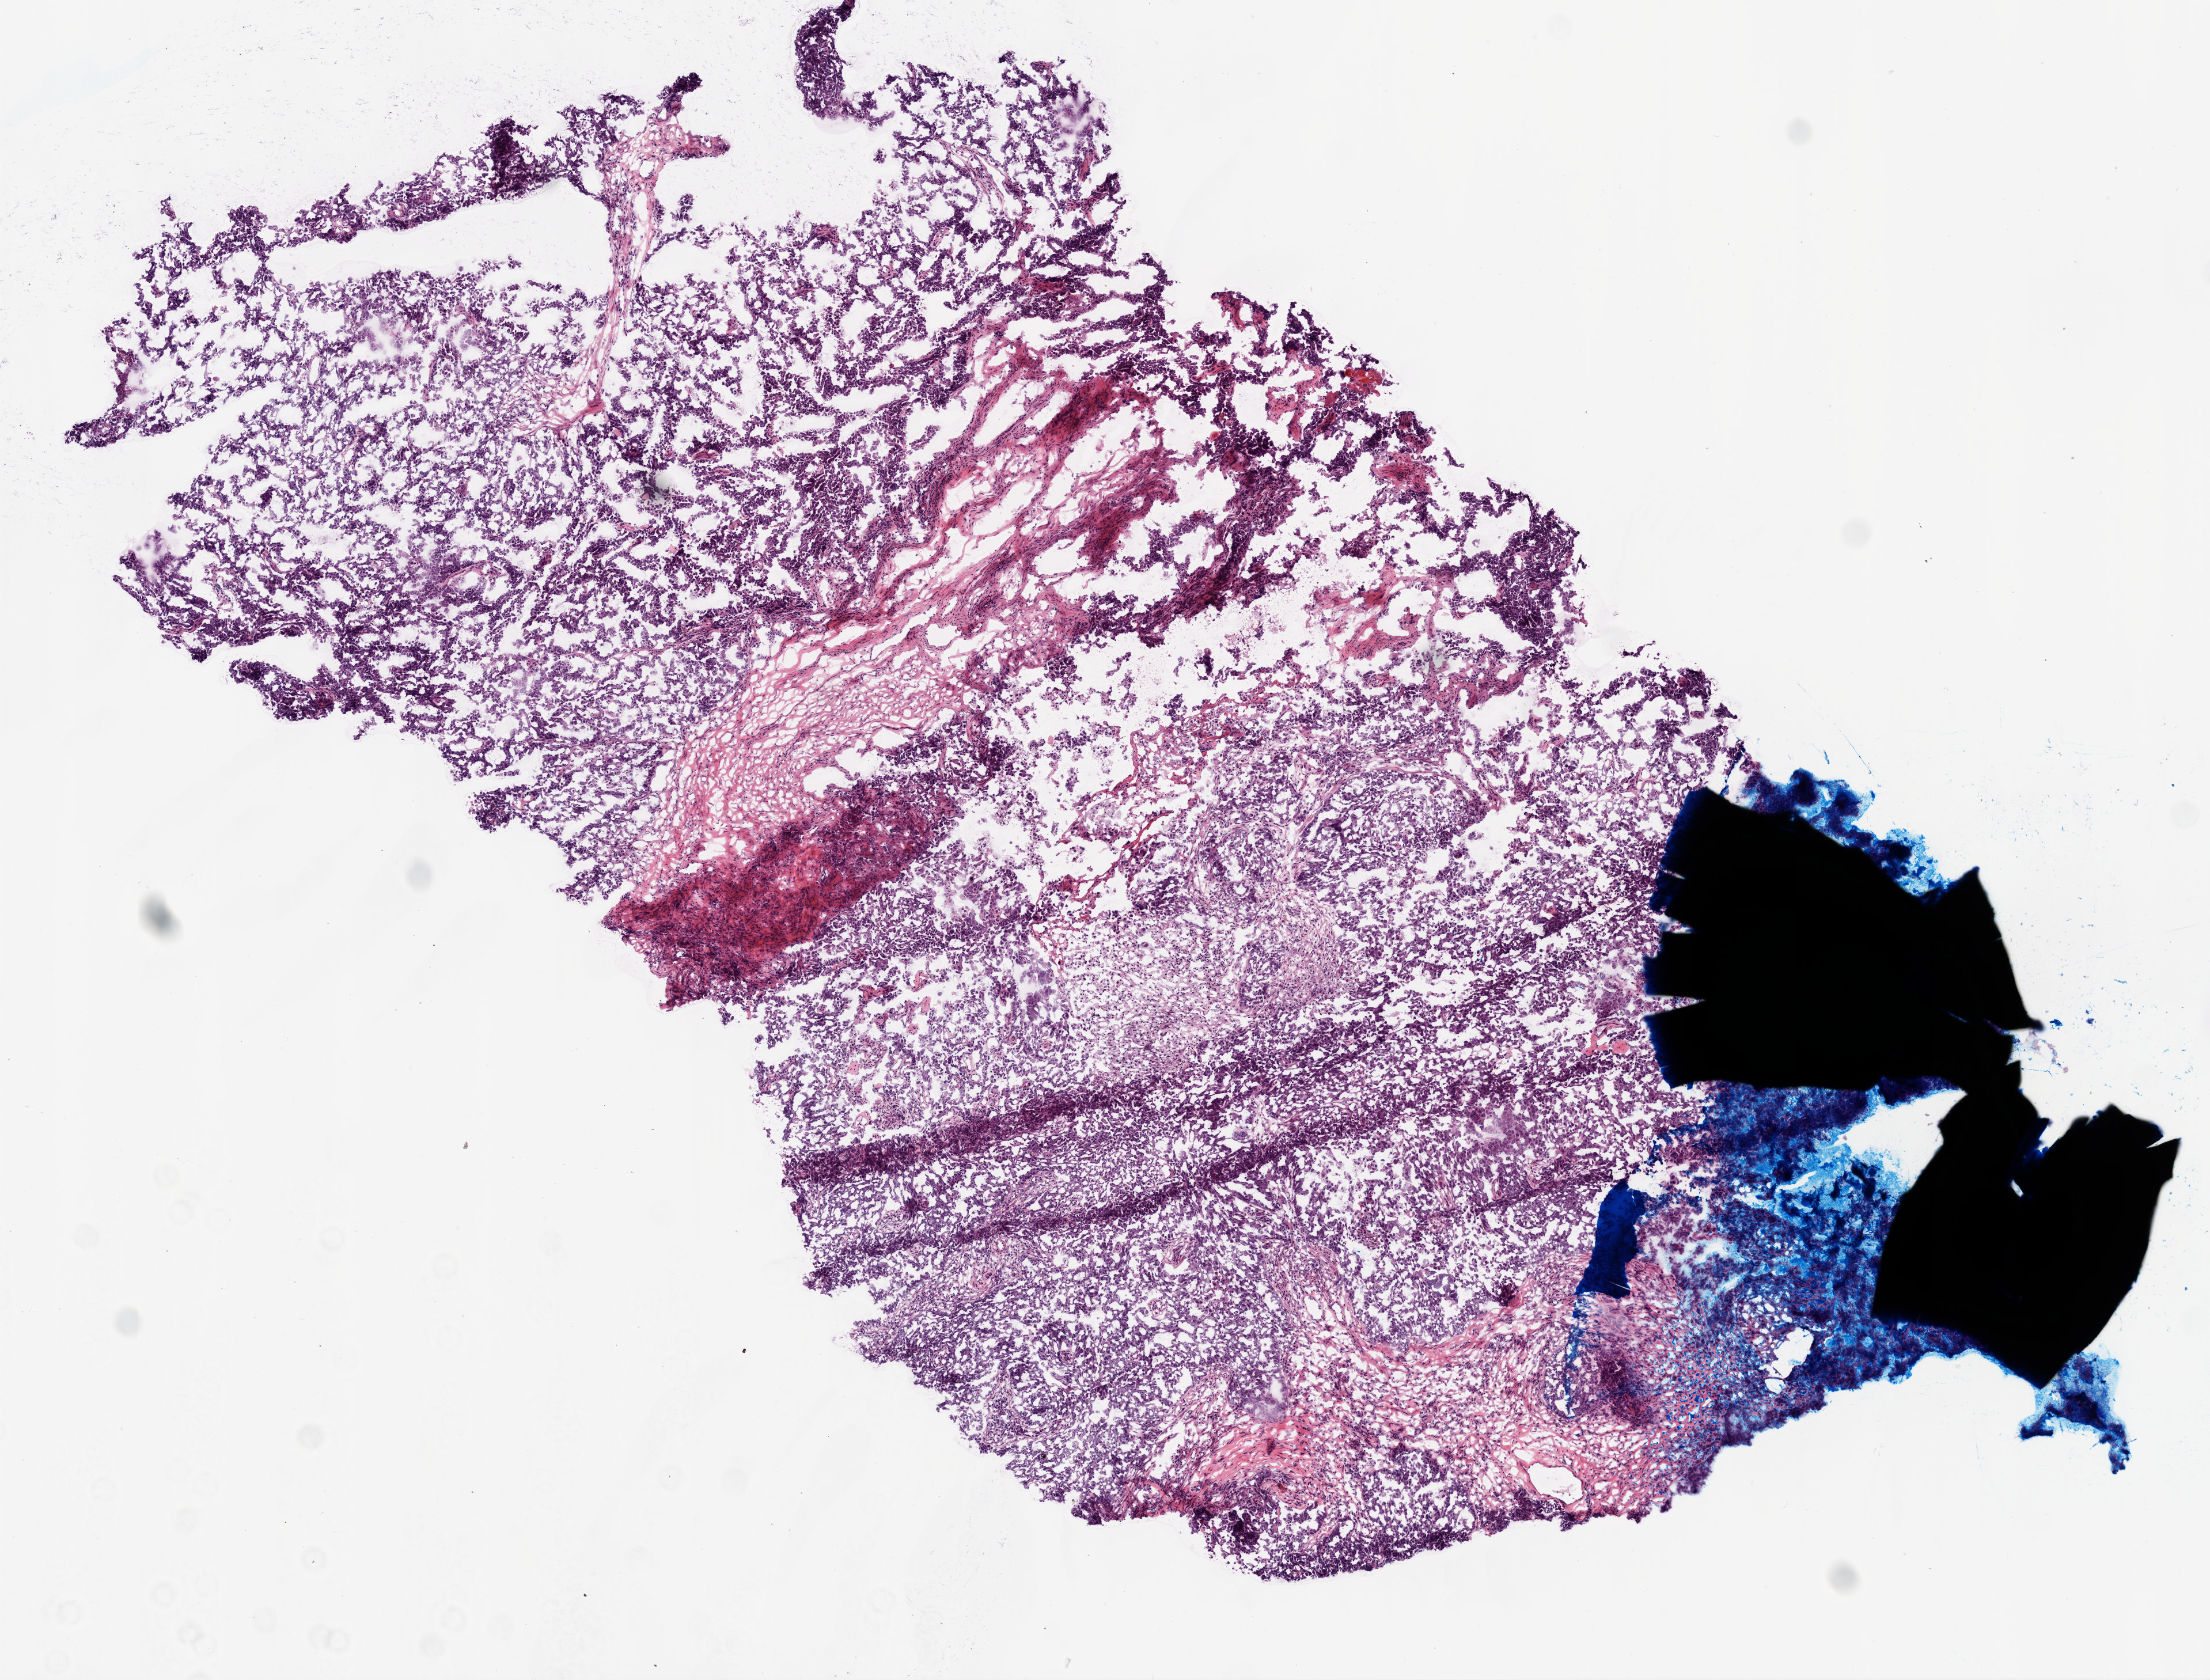
H&E whole-slide image, whole scanned area (about 7.7 x 5.9 mm) shown as a low-resolution overview, frozen section from the top of the tissue portion, ovary, primary tumour sample. Female, age 59 years at initial diagnosis. Histologic grade: G3 (poorly differentiated). Pathologist review of this section (percent, as recorded): tumour cells 0%, tumour nuclei 90%, normal cells 0%, stromal cells 0%, necrosis 5%.
Pathologic diagnosis: Serous cystadenocarcinoma, NOS. FIGO stage: IV. Laterality: left.